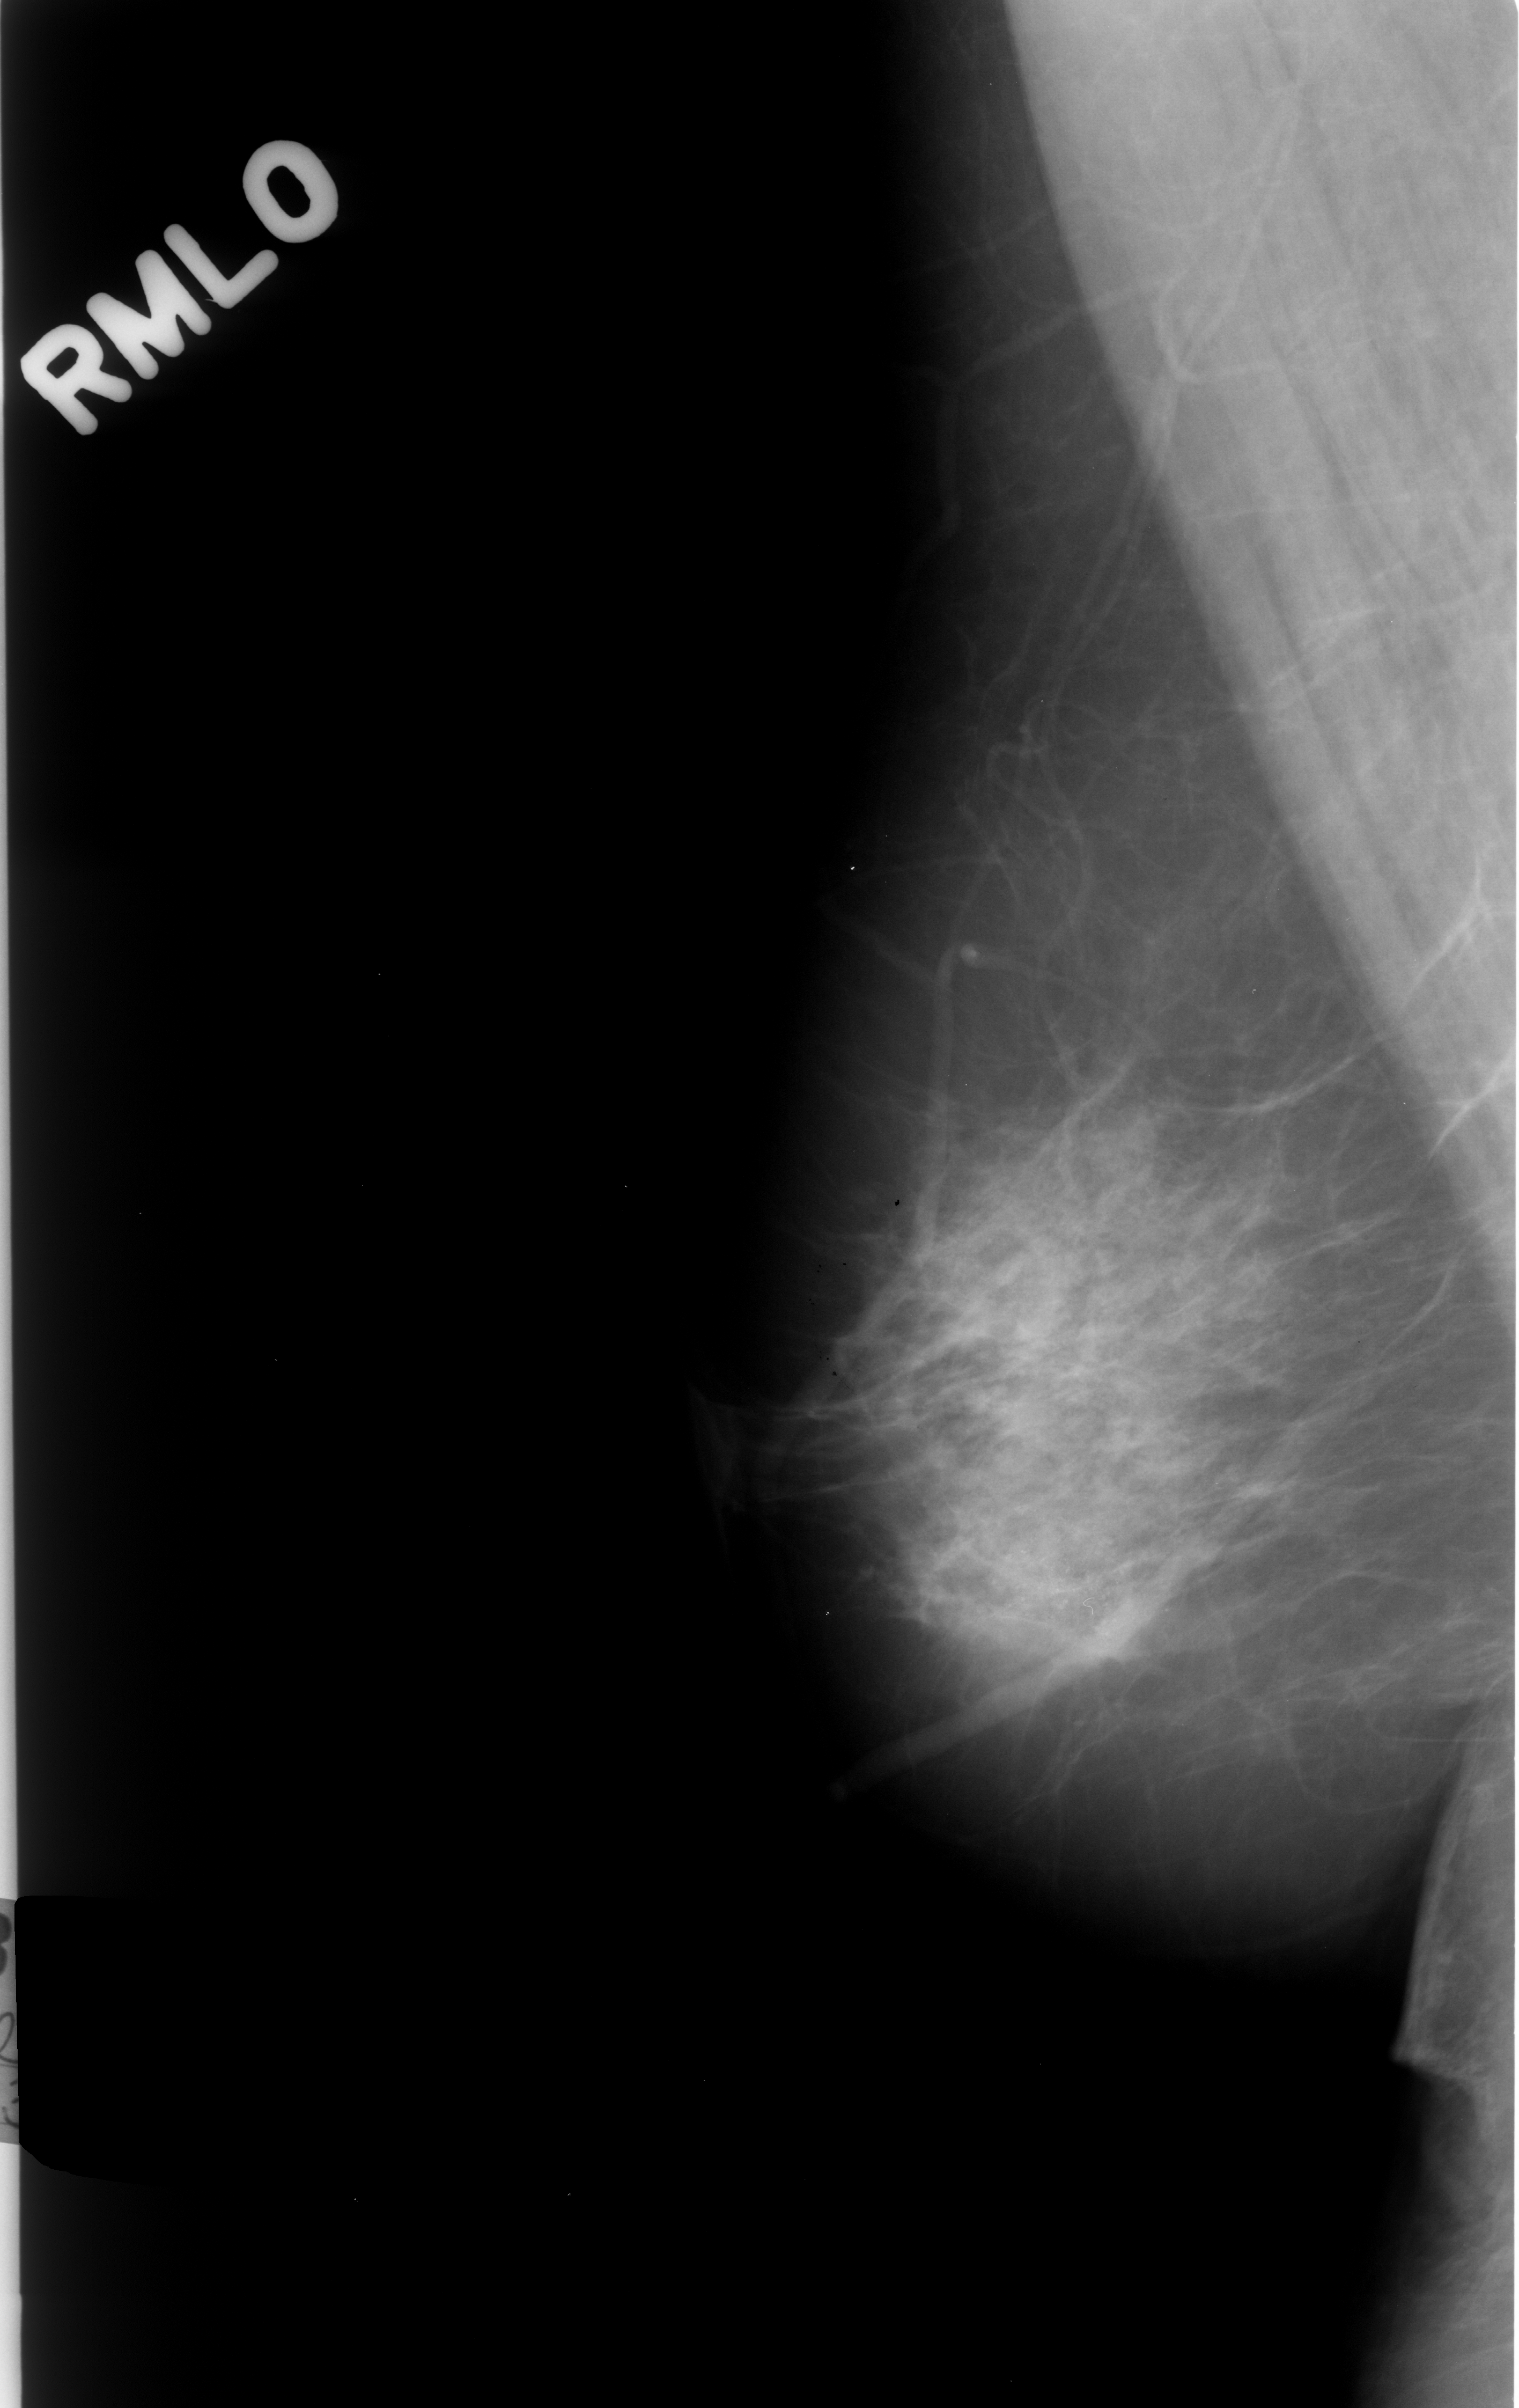
Digitized screen-film mammogram; right breast; MLO view; 1519 × 2408 image matrix.
Expert-marked regions of interest on this image (one box per marked abnormality):
- calcifications, morphology amorphous, distribution clustered; BI-RADS assessment category 4; subtlety rating 3 on a 1 (subtle) to 5 (obvious) scale; pathology result (as recorded, not read from the image): benign: bounding box (x1, y1, x2, y2) in pixels: (939, 1506, 1215, 1748)